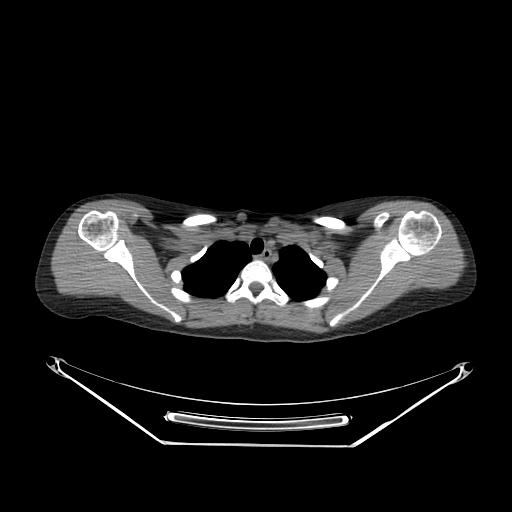
CT of an extremity soft-tissue mass (from a PET/CT study), one axial slice; position 214 of 267 along the scan axis; reconstruction kernel SOFT; soft-tissue window (W 400 / L 40 HU); 3.75 mm slice thickness; 512 × 512 image matrix, field of view 500 × 500 mm. Female patient. From the clinical record (not read from this slice): histological type: malignant fibrous histiocytoma; grade: low; site of the primary tumour: left arm.
Outlined on this slice (expert contour drawn on MRI and transferred to this co-registered scan by the dataset authors):
- gross tumour volume (mass): bounding box <425,267,442,277> (left, top, right, bottom; pixels)